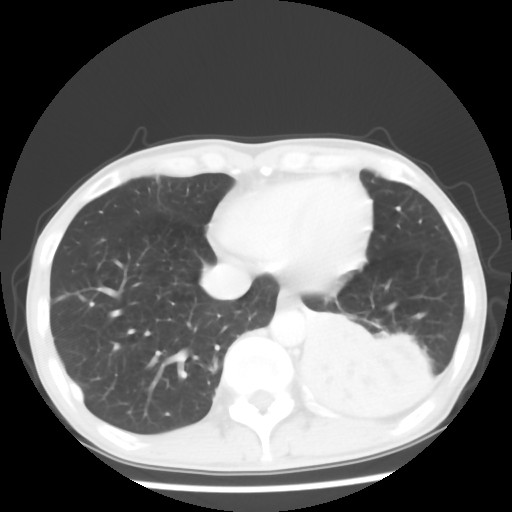
Chest CT, one axial slice. Slice 15 of 64 in the series (ordered by position). Reconstruction kernel STANDARD. Lung window (W 1500 / L -600 HU). 5 mm slice thickness. 512 × 512 image matrix. Patient: male, 68 years. Case-level facts recorded for this patient, not image findings: clinical TNM (as recorded): T4 N0 M0.
Outlined on this slice (rectangle marked by the reading radiologist):
- lung tumour (recorded histology: squamous cell carcinoma): bounding box [x1, y1, x2, y2] px = [287, 314, 437, 431]